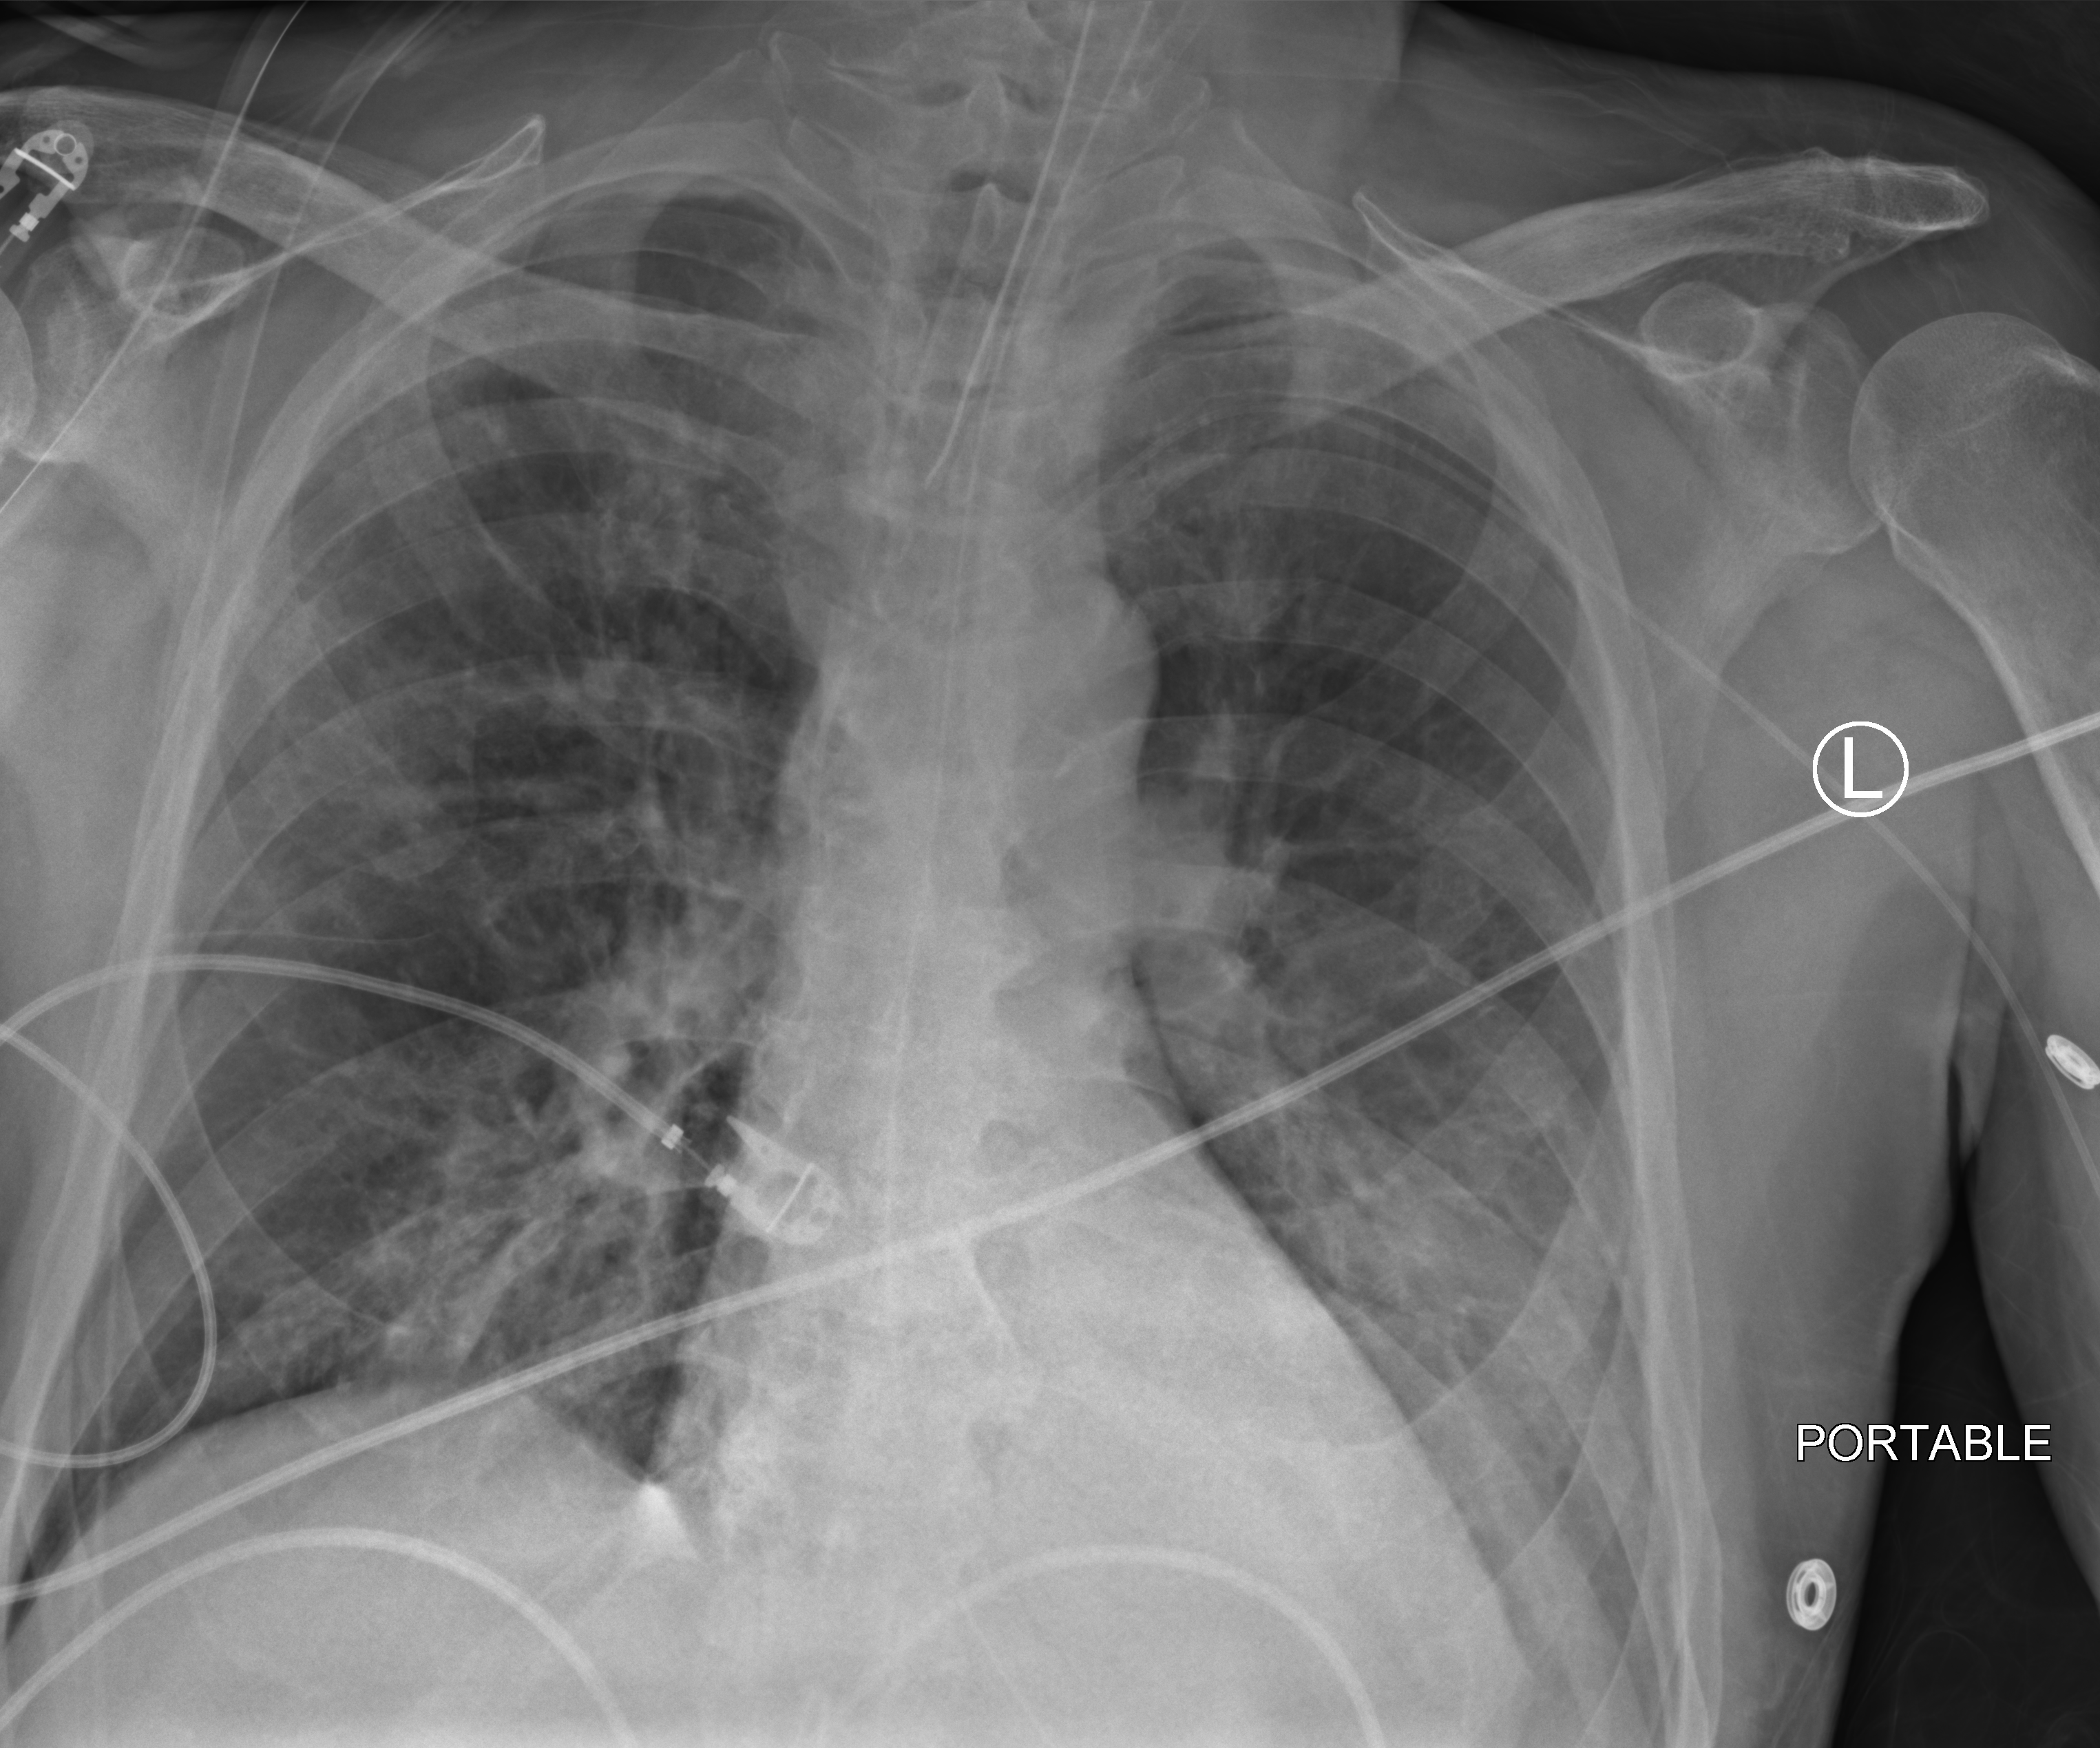
Portable chest radiograph, anteroposterior (AP) projection. Patient hospitalised with COVID-19; male, aged 60–74 years.
Hospital-stay facts (about this admission, not read from this image; timing relative to this image not recorded): other chronic lung disease (admission record): no.